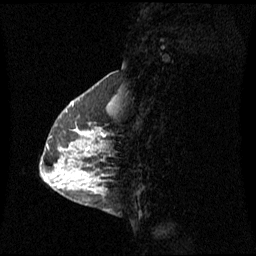
Breast MRI (dynamic contrast-enhanced), one sagittal slice; slice 20 of 60 in the series (ordered by position); dynamic contrast-enhanced series, image 2 of 3 at this slice position (ordered by acquisition); 1.5 T; TE 4.2 ms, TR 8.4 ms; 2 mm slice thickness; 256 × 256 image matrix, field of view 270 × 270 mm. Female patient, age 42 years. Case-level facts recorded for this patient, not image findings: setting: breast cancer imaged before/during neoadjuvant chemotherapy; receptor status: HR-positive, HER2-negative.
Annotated regions visible in this slice (semi-automatic segmentation, software-assisted and operator-edited):
- analysis volume of interest (the breast-tissue region the enhancement analysis was run in; not a lesion): box from (x=56, y=104) to (x=113, y=185) px
- tumour enhancement mask (voxels above the 70 % enhancement threshold inside the analysis volume of interest): (x=101, y=133)–(x=103, y=135)